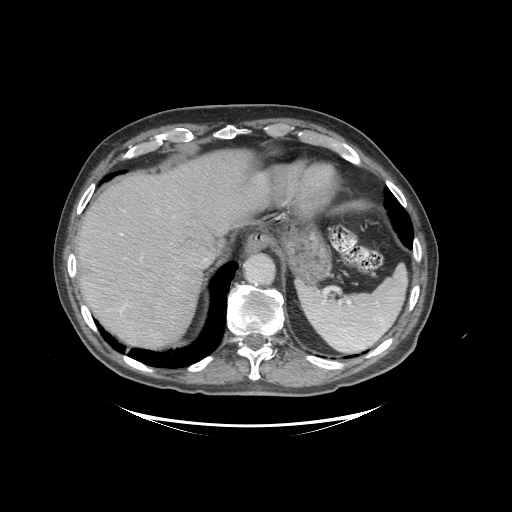
Contrast-enhanced abdominal CT (liver protocol), one axial slice. Slice 79 of 99 in the series (ordered by position). Soft-tissue window (W 400 / L 40 HU). 2.5 mm slice thickness. 512 × 512 image matrix, field of view 460 × 460 mm. From the clinical record (not read from this slice): diagnosis: hepatocellular carcinoma (patient treated with transarterial chemoembolisation; whether this scan precedes or follows treatment is not stated here); TNM stage (as recorded): Stage-I; Child-Pugh class: A; tumour differentiation: moderately differentiated; tumour nodularity: uninodular.
Annotated regions visible in this slice (semi-automatic segmentation, software-assisted and operator-edited):
- liver parenchyma outside the tumour (the mass and vessels are separate outlines, so this box may not span the whole liver): box from (x=76, y=150) to (x=270, y=348) px
- liver vessels: (x=120, y=233)–(x=208, y=312)